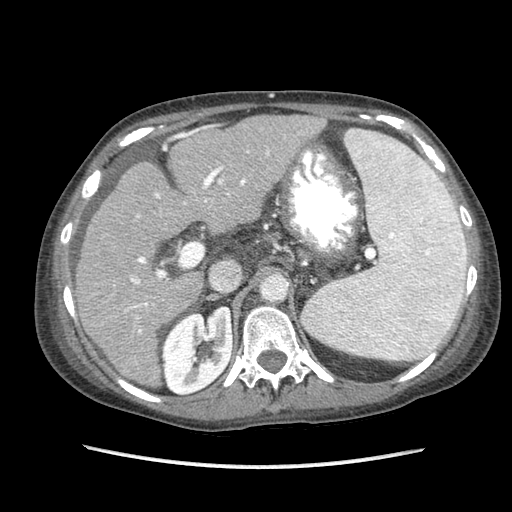
Contrast-enhanced abdominal CT (liver protocol), one axial slice. Position 52 of 87 along the scan axis. Soft-tissue window (W 400 / L 40 HU). 512 × 512 image matrix, field of view 340 × 340 mm. From the clinical record (not read from this slice): diagnosis: hepatocellular carcinoma (patient treated with transarterial chemoembolisation; whether this scan precedes or follows treatment is not stated here); TNM stage (as recorded): Stage-IIIB; Child-Pugh class: A; tumour differentiation: no biopsy; tumour nodularity: uninodular.
Annotated regions visible in this slice (semi-automatic segmentation, software-assisted and operator-edited):
- liver parenchyma outside the tumour (the mass and vessels are separate outlines, so this box may not span the whole liver): bounding box (x1, y1, x2, y2) in pixels: (75, 114, 403, 386)
- liver vessels: (125, 125, 402, 333)